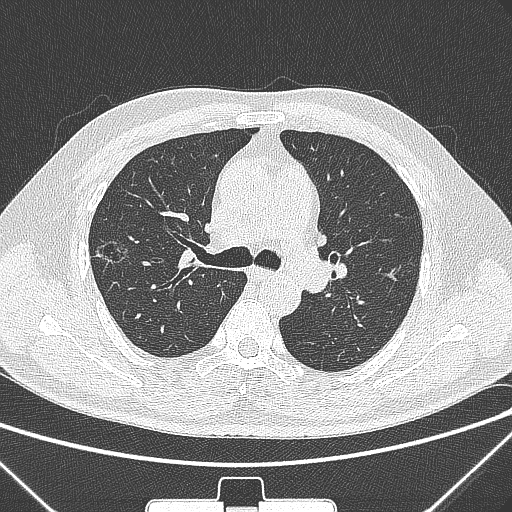
Chest CT, one axial slice; position 198 of 320 along the scan axis; lung window (W 1500 / L -600 HU); 512 × 512 image matrix, field of view 350 × 350 mm. Male patient, age 58 years. Case-level facts recorded for this patient, not image findings: clinical TNM (as recorded): T1c N0 M0.
Outlined on this slice (rectangle marked by the reading radiologist):
- lung tumour (recorded histology: adenocarcinoma): box from (x=90, y=228) to (x=139, y=272) px